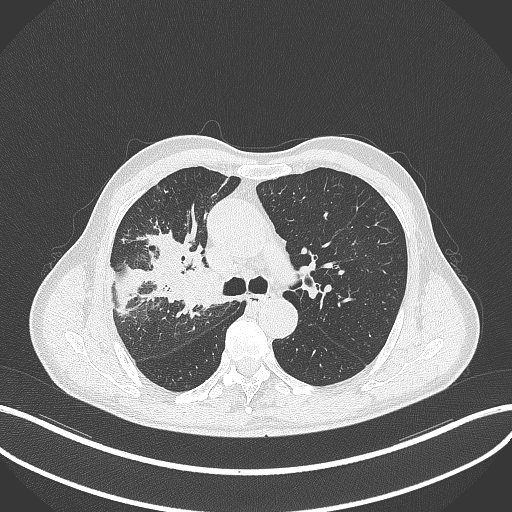
Chest CT, one axial slice. Slice 322 of 490 in the series (ordered by position). 120 kVp. Lung window (W 1500 / L -600 HU). 512 × 512 image matrix. Male patient, age 69 years. From the clinical record (not read from this slice): clinical TNM (as recorded): T2a N0 M0.
Annotated regions visible in this slice (bounding box drawn by a radiologist):
- lung tumour (recorded histology: adenocarcinoma): bounding box (x1, y1, x2, y2) in pixels: (180, 256, 222, 312)